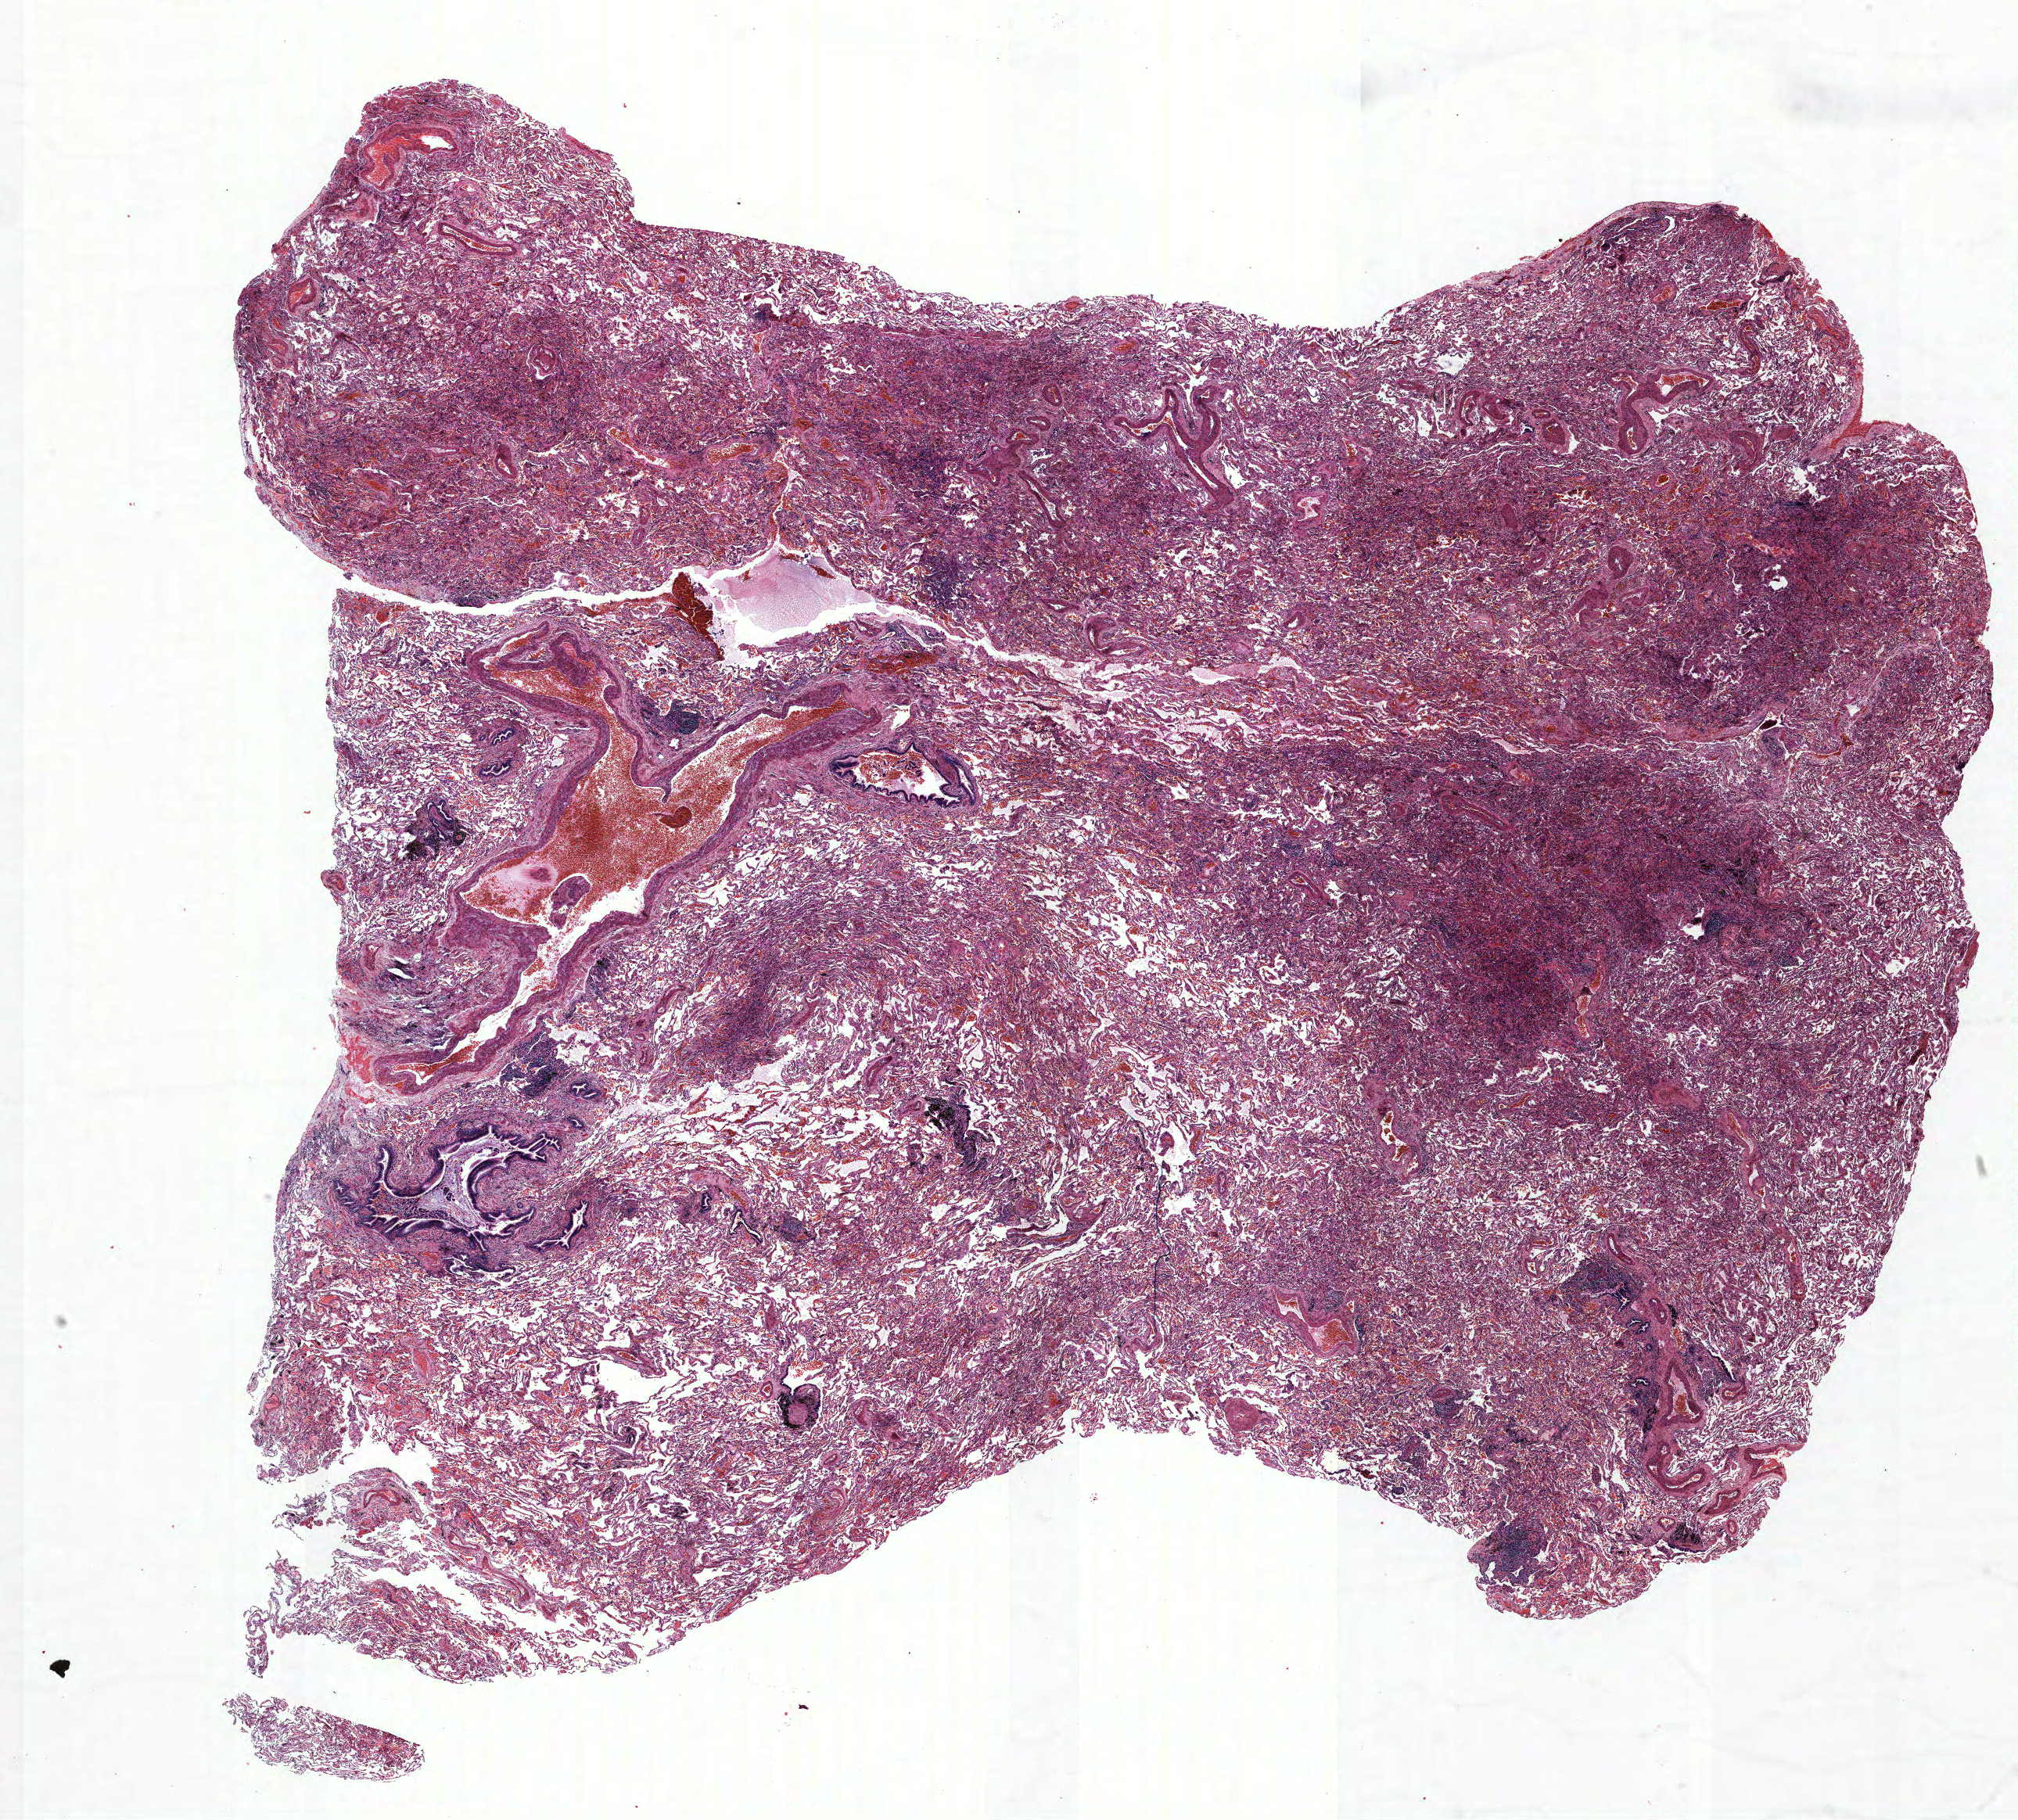
Whole-slide histology image, H&E-stained — whole scanned area (about 20.6 x 18.6 mm) shown as a low-resolution overview, FFPE section, lung tissue. Male patient, aged 64 at enrolment. Former smoker at enrolment. Grade: poorly differentiated (G3).
Tumour size (pathology): 11 mm. Primary tumour location (clinical record): right upper lobe. Participant's lung-cancer diagnosis: Adenocarcinoma, NOS. Stage (AJCC 6th edition): IA.